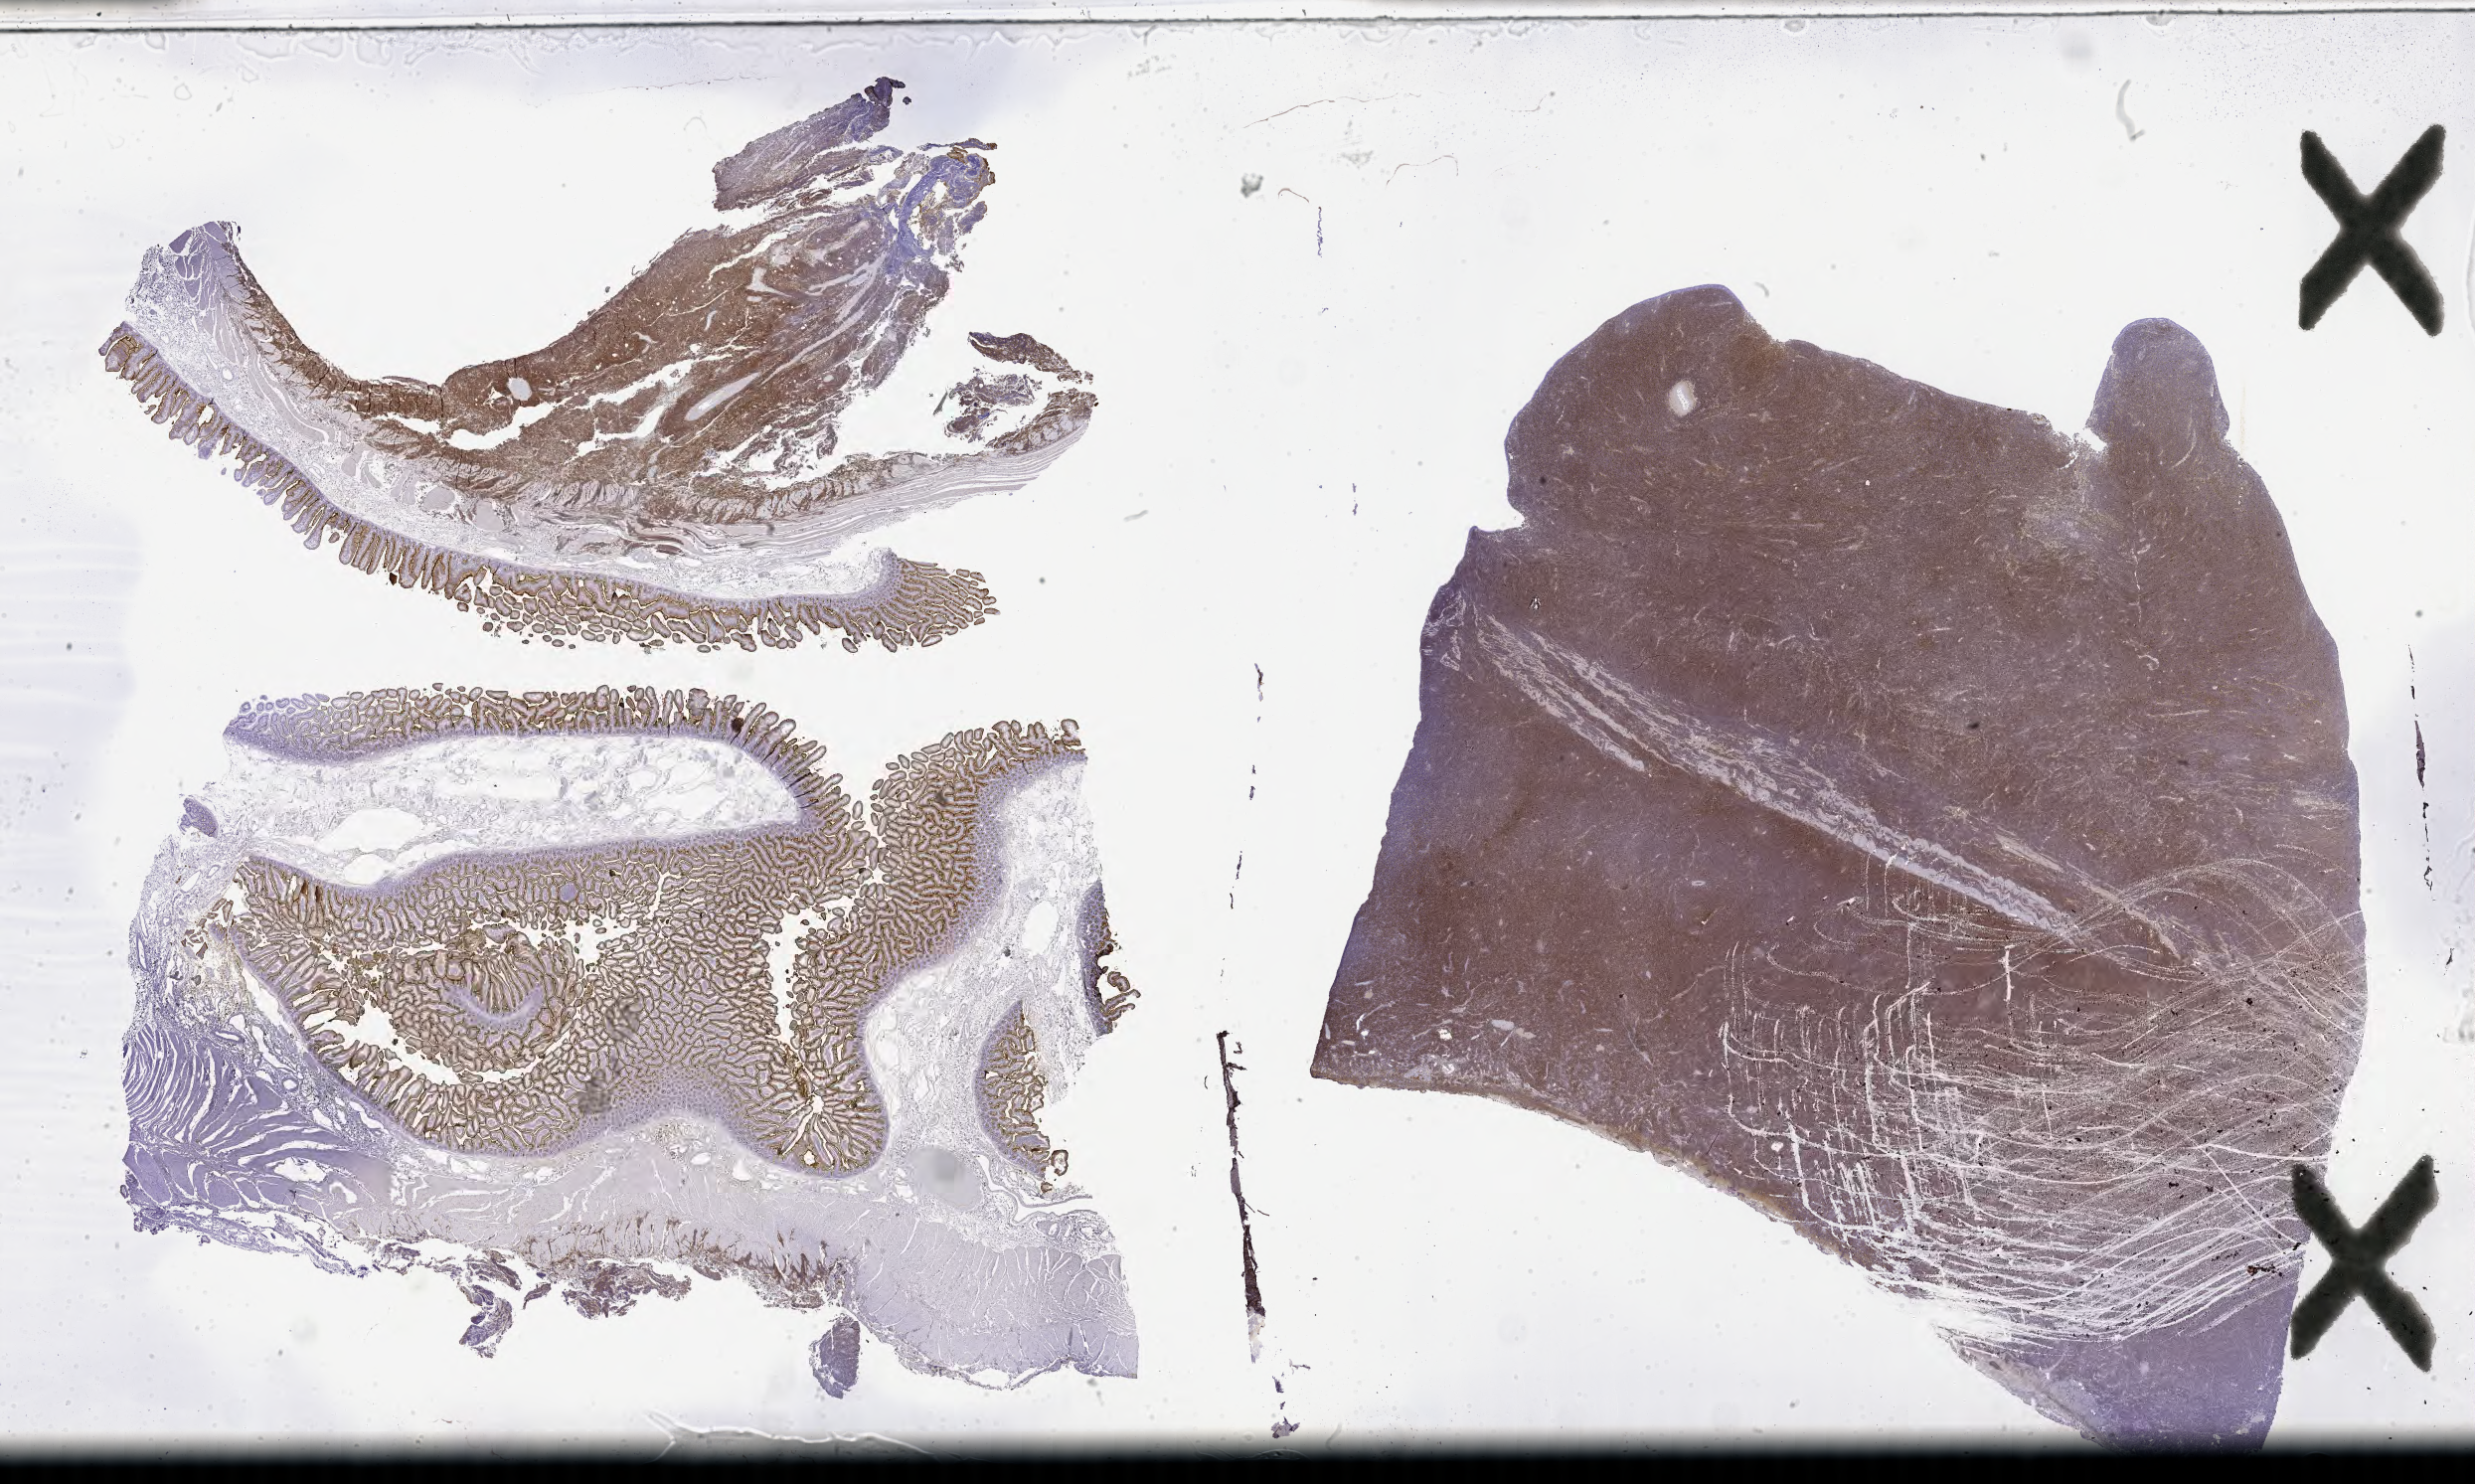
IHC for CD10, whole-slide image, shown as a low-resolution overview of the whole scanned area (about 40.2 x 24.1 mm), specimen: tumor tissue. Male patient, age 36 years.
Histologic diagnosis: Burkitt lymphoma, NOS.